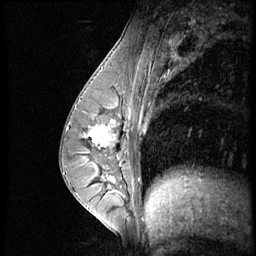
Breast MRI (dynamic contrast-enhanced), one sagittal slice. Slice 27 of 56 in the series (ordered by position). Dynamic contrast-enhanced series, image 2 of 4 at this slice position (ordered by acquisition). 1.5 T. TE 4.2 ms, TR 8.9 ms. 256 × 256 image matrix, field of view 200 × 200 mm. Female patient, age 35 years. Case-level facts recorded for this patient, not image findings: setting: breast cancer imaged before/during neoadjuvant chemotherapy; receptor status: HER2-positive.
Outlined on this slice (semi-automatically segmented with operator editing):
- analysis volume of interest (the breast-tissue region the enhancement analysis was run in; not a lesion): box from (x=73, y=111) to (x=131, y=164) px
- tumour enhancement mask (voxels above the 140 % enhancement threshold inside the analysis volume of interest): (x=78, y=121)–(x=116, y=164)